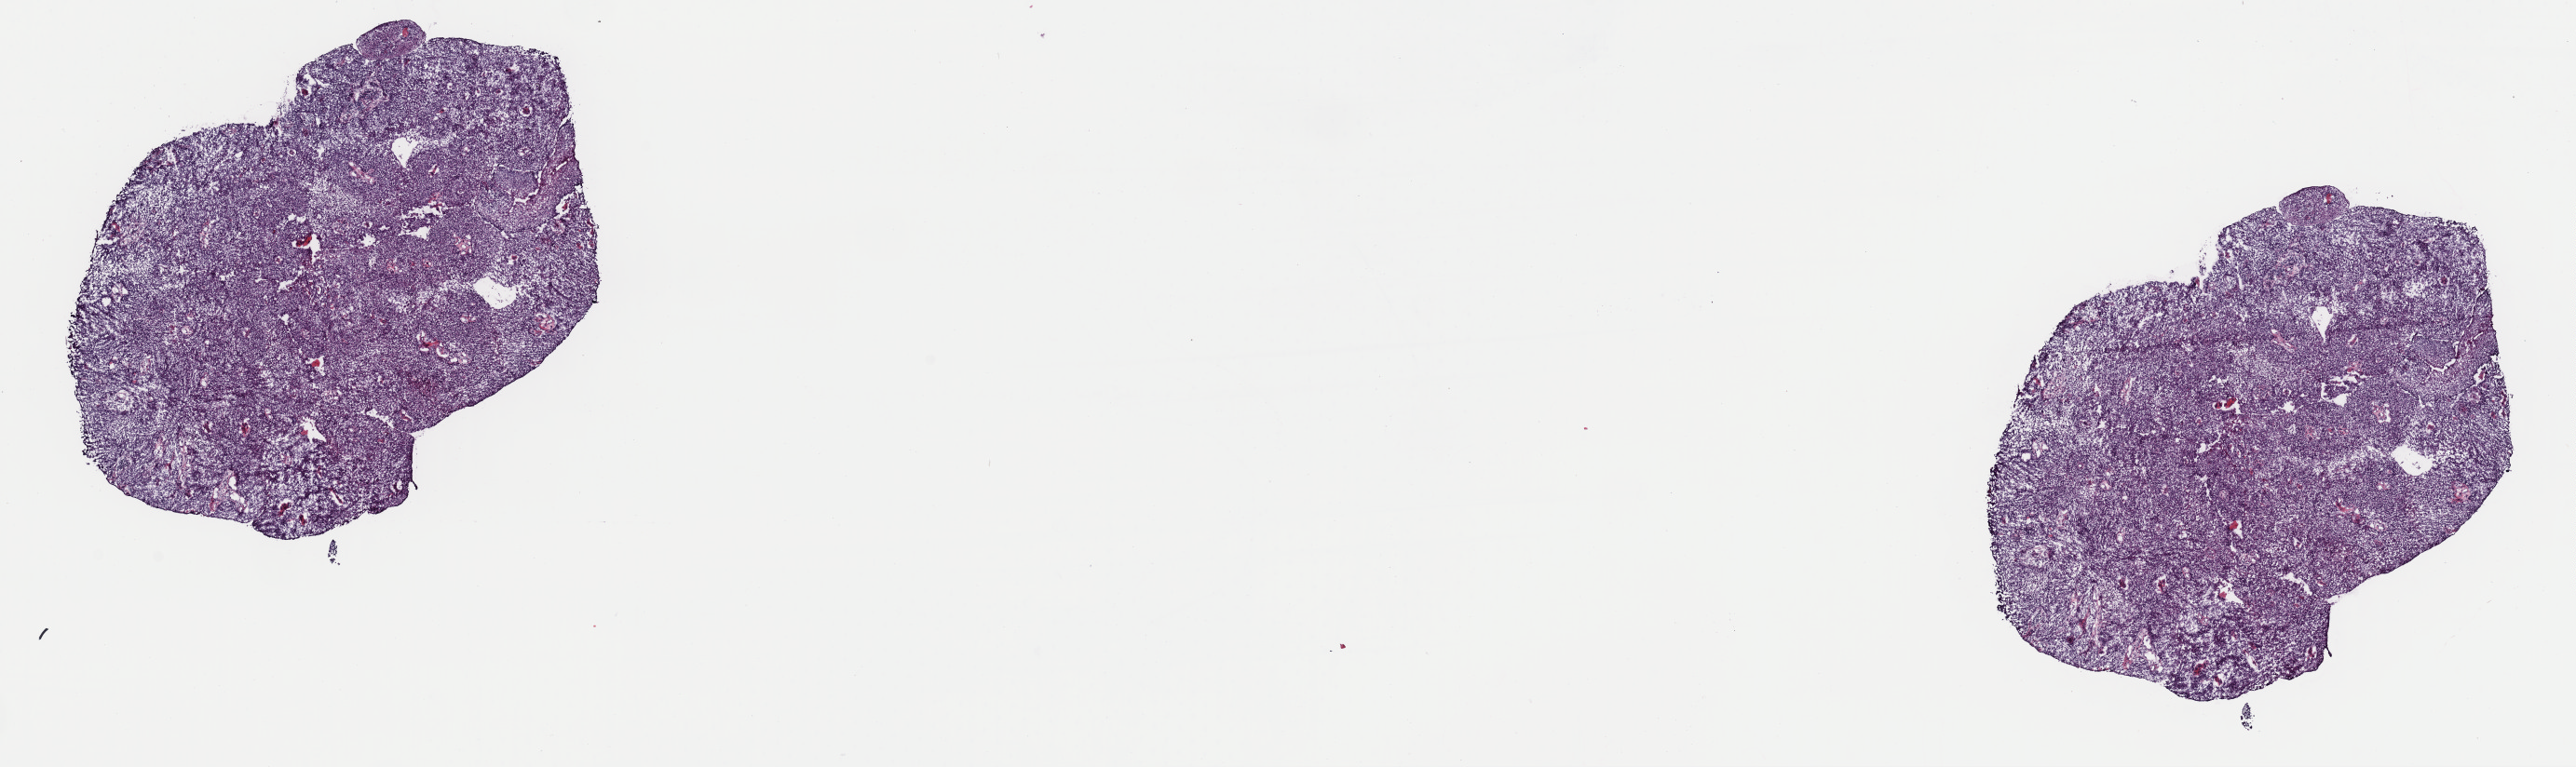
Digitized H&E-stained tissue section (whole slide) — whole scanned area (about 21.9 x 6.5 mm) shown as a low-resolution overview, frozen section from the top of the tissue portion, head and neck, primary tumour sample. Male patient; age at initial diagnosis 67 years. Histologic grade: GX (grade cannot be assessed). Pathologist review of this section (percent, as recorded): tumour cells 100%, tumour nuclei 95%, normal cells 0%, stromal cells 0%, necrosis 0%. Infiltration values recorded for this section: lymphocyte infiltration 0%, monocyte infiltration 0%, neutrophil infiltration 0%.
- diagnosis: Squamous cell carcinoma, large cell, nonkeratinizing, NOS (tonsil, NOS)
- laterality: right